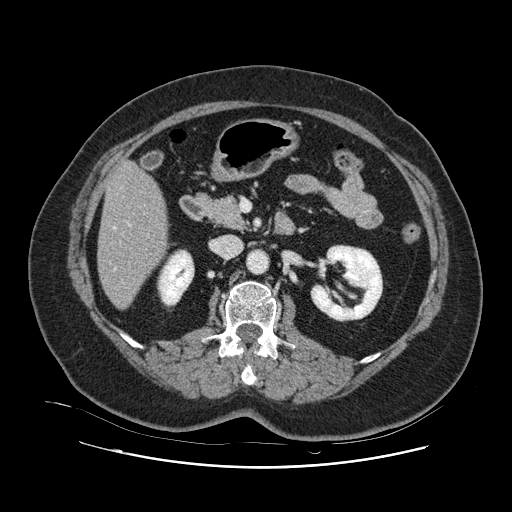
Contrast-enhanced abdominal CT, one axial slice. Slice 38 of 132 in the series (ordered by position). Intravenous contrast given. Soft-tissue window (W 400 / L 40 HU). 2.5 mm slice thickness. 512 × 512 image matrix, field of view 391 × 391 mm. Female patient, age 73 years. Case-level facts recorded for this patient, not image findings: diagnosis: colorectal cancer liver metastases, imaged before liver resection; multiple liver metastases: no; largest metastasis: 7 cm.
Annotated regions visible in this slice (expert manual segmentation):
- hepatic veins: bounding box [x1, y1, x2, y2] px = [114, 226, 116, 271]
- liver: [98, 163, 166, 308]
- planned liver remnant (the part of the liver to remain after resection): [98, 163, 166, 308]